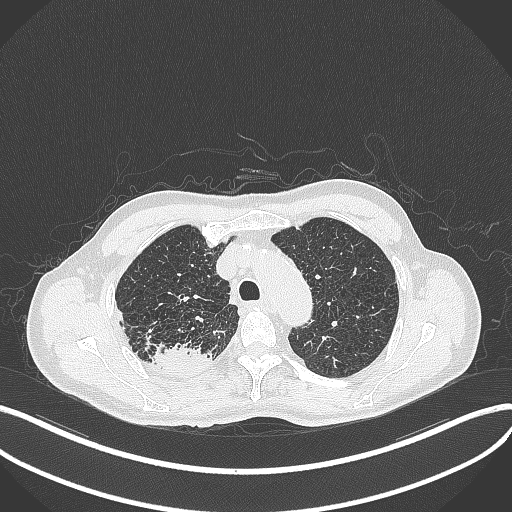
Chest CT, one axial slice. Position 343 of 428 along the scan axis. 120 kVp. Lung window (W 1500 / L -600 HU). 1 mm slice thickness. 512 × 512 image matrix. Male patient, age 79 years. From the clinical record (not read from this slice): clinical TNM (as recorded): T3 N0 M0.
Annotated regions visible in this slice (rectangle marked by the reading radiologist):
- lung tumour (recorded histology: adenocarcinoma): box from (x=149, y=341) to (x=214, y=375) px